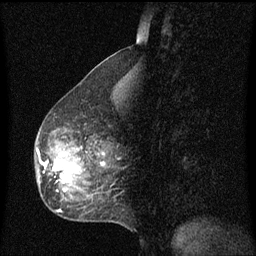
Breast MRI (dynamic contrast-enhanced), one sagittal slice; slice 28 of 60 in the series (ordered by position); dynamic contrast-enhanced series, image 2 of 3 at this slice position (ordered by acquisition); 1.5 T; TE 4.2 ms, TR 8.4 ms; 2 mm slice thickness; 256 × 256 image matrix, field of view 200 × 200 mm. Female patient, age 49 years. Case-level facts recorded for this patient, not image findings: setting: breast cancer imaged before/during neoadjuvant chemotherapy; receptor status: HR-positive, HER2-negative.
Structures marked on this image (semi-automatic segmentation, software-assisted and operator-edited):
- analysis volume of interest (the breast-tissue region the enhancement analysis was run in; not a lesion): bounding box <36,128,115,201> (left, top, right, bottom; pixels)
- tumour enhancement mask (voxels above the 70 % enhancement threshold inside the analysis volume of interest): <46,154,79,183>